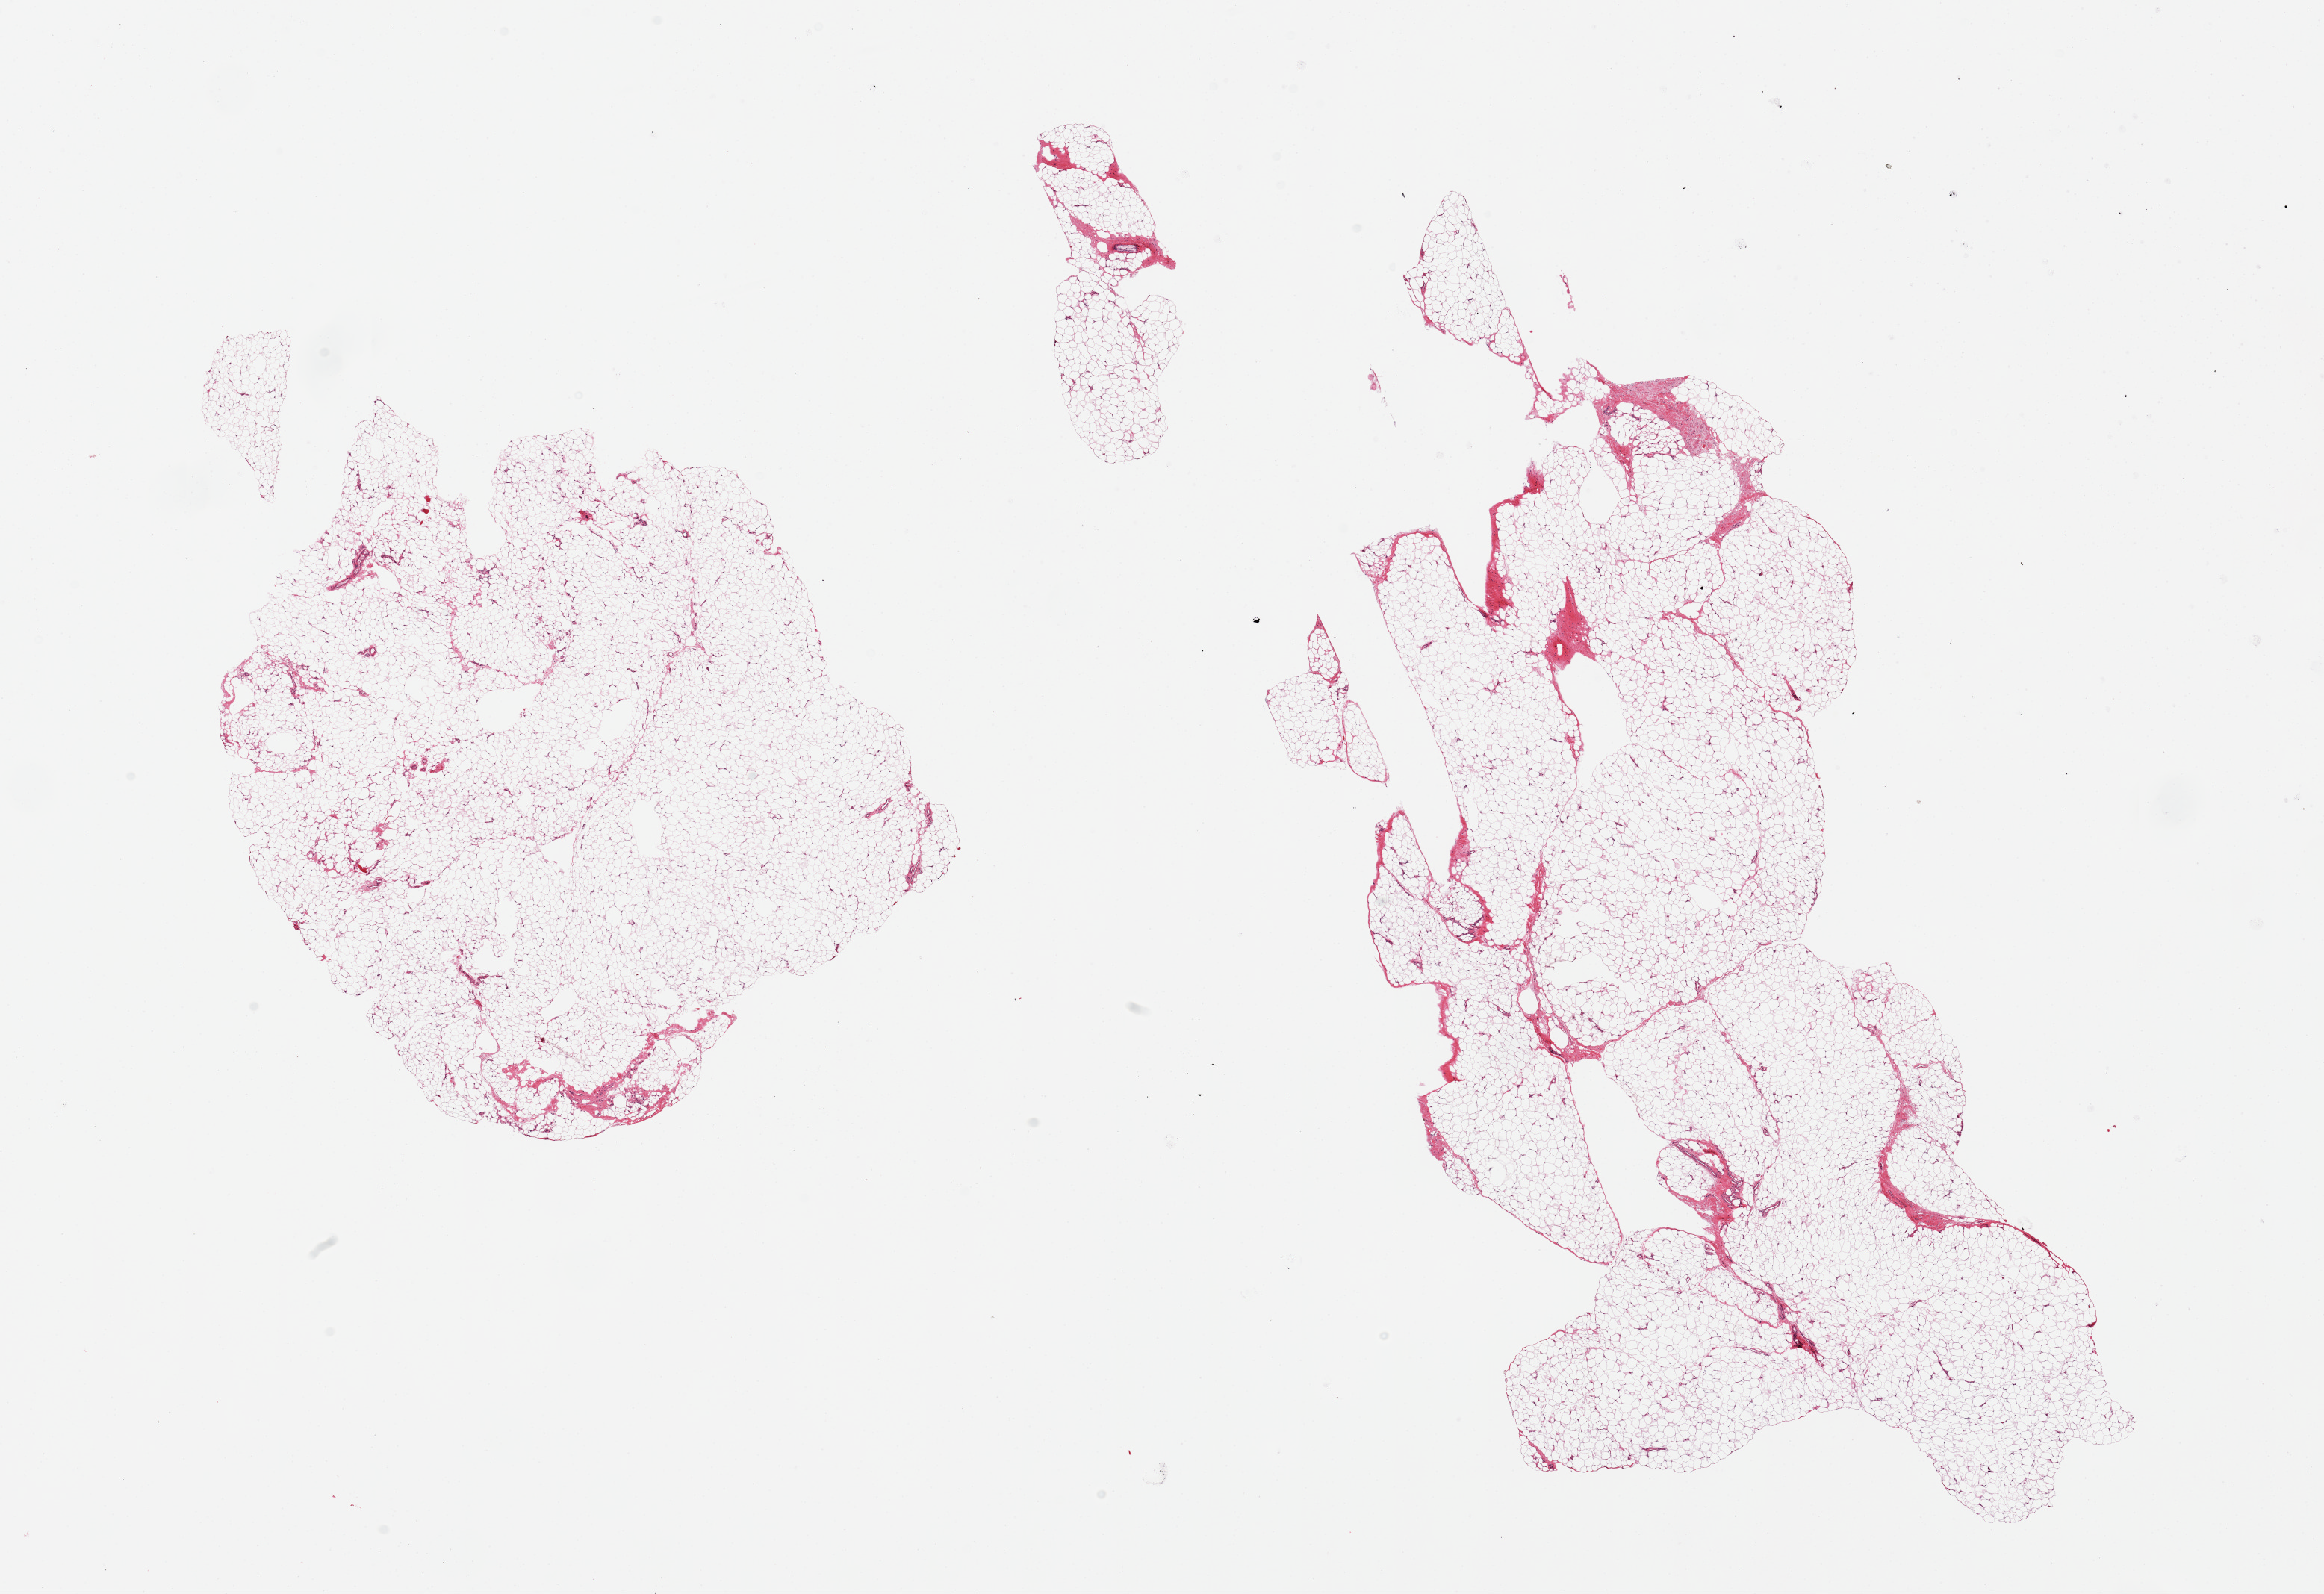
Haematoxylin and eosin whole-slide image, a low-resolution overview of the entire scanned area, about 24.6 x 16.9 mm. PAXgene-fixed paraffin-embedded (PFPE) section. Target tissue: adipose tissue. Donor tissue sample. Female donor.
Pathologist's review note for this sample: 2 pieces; small amounts of interstitial fibrovascular tissue.